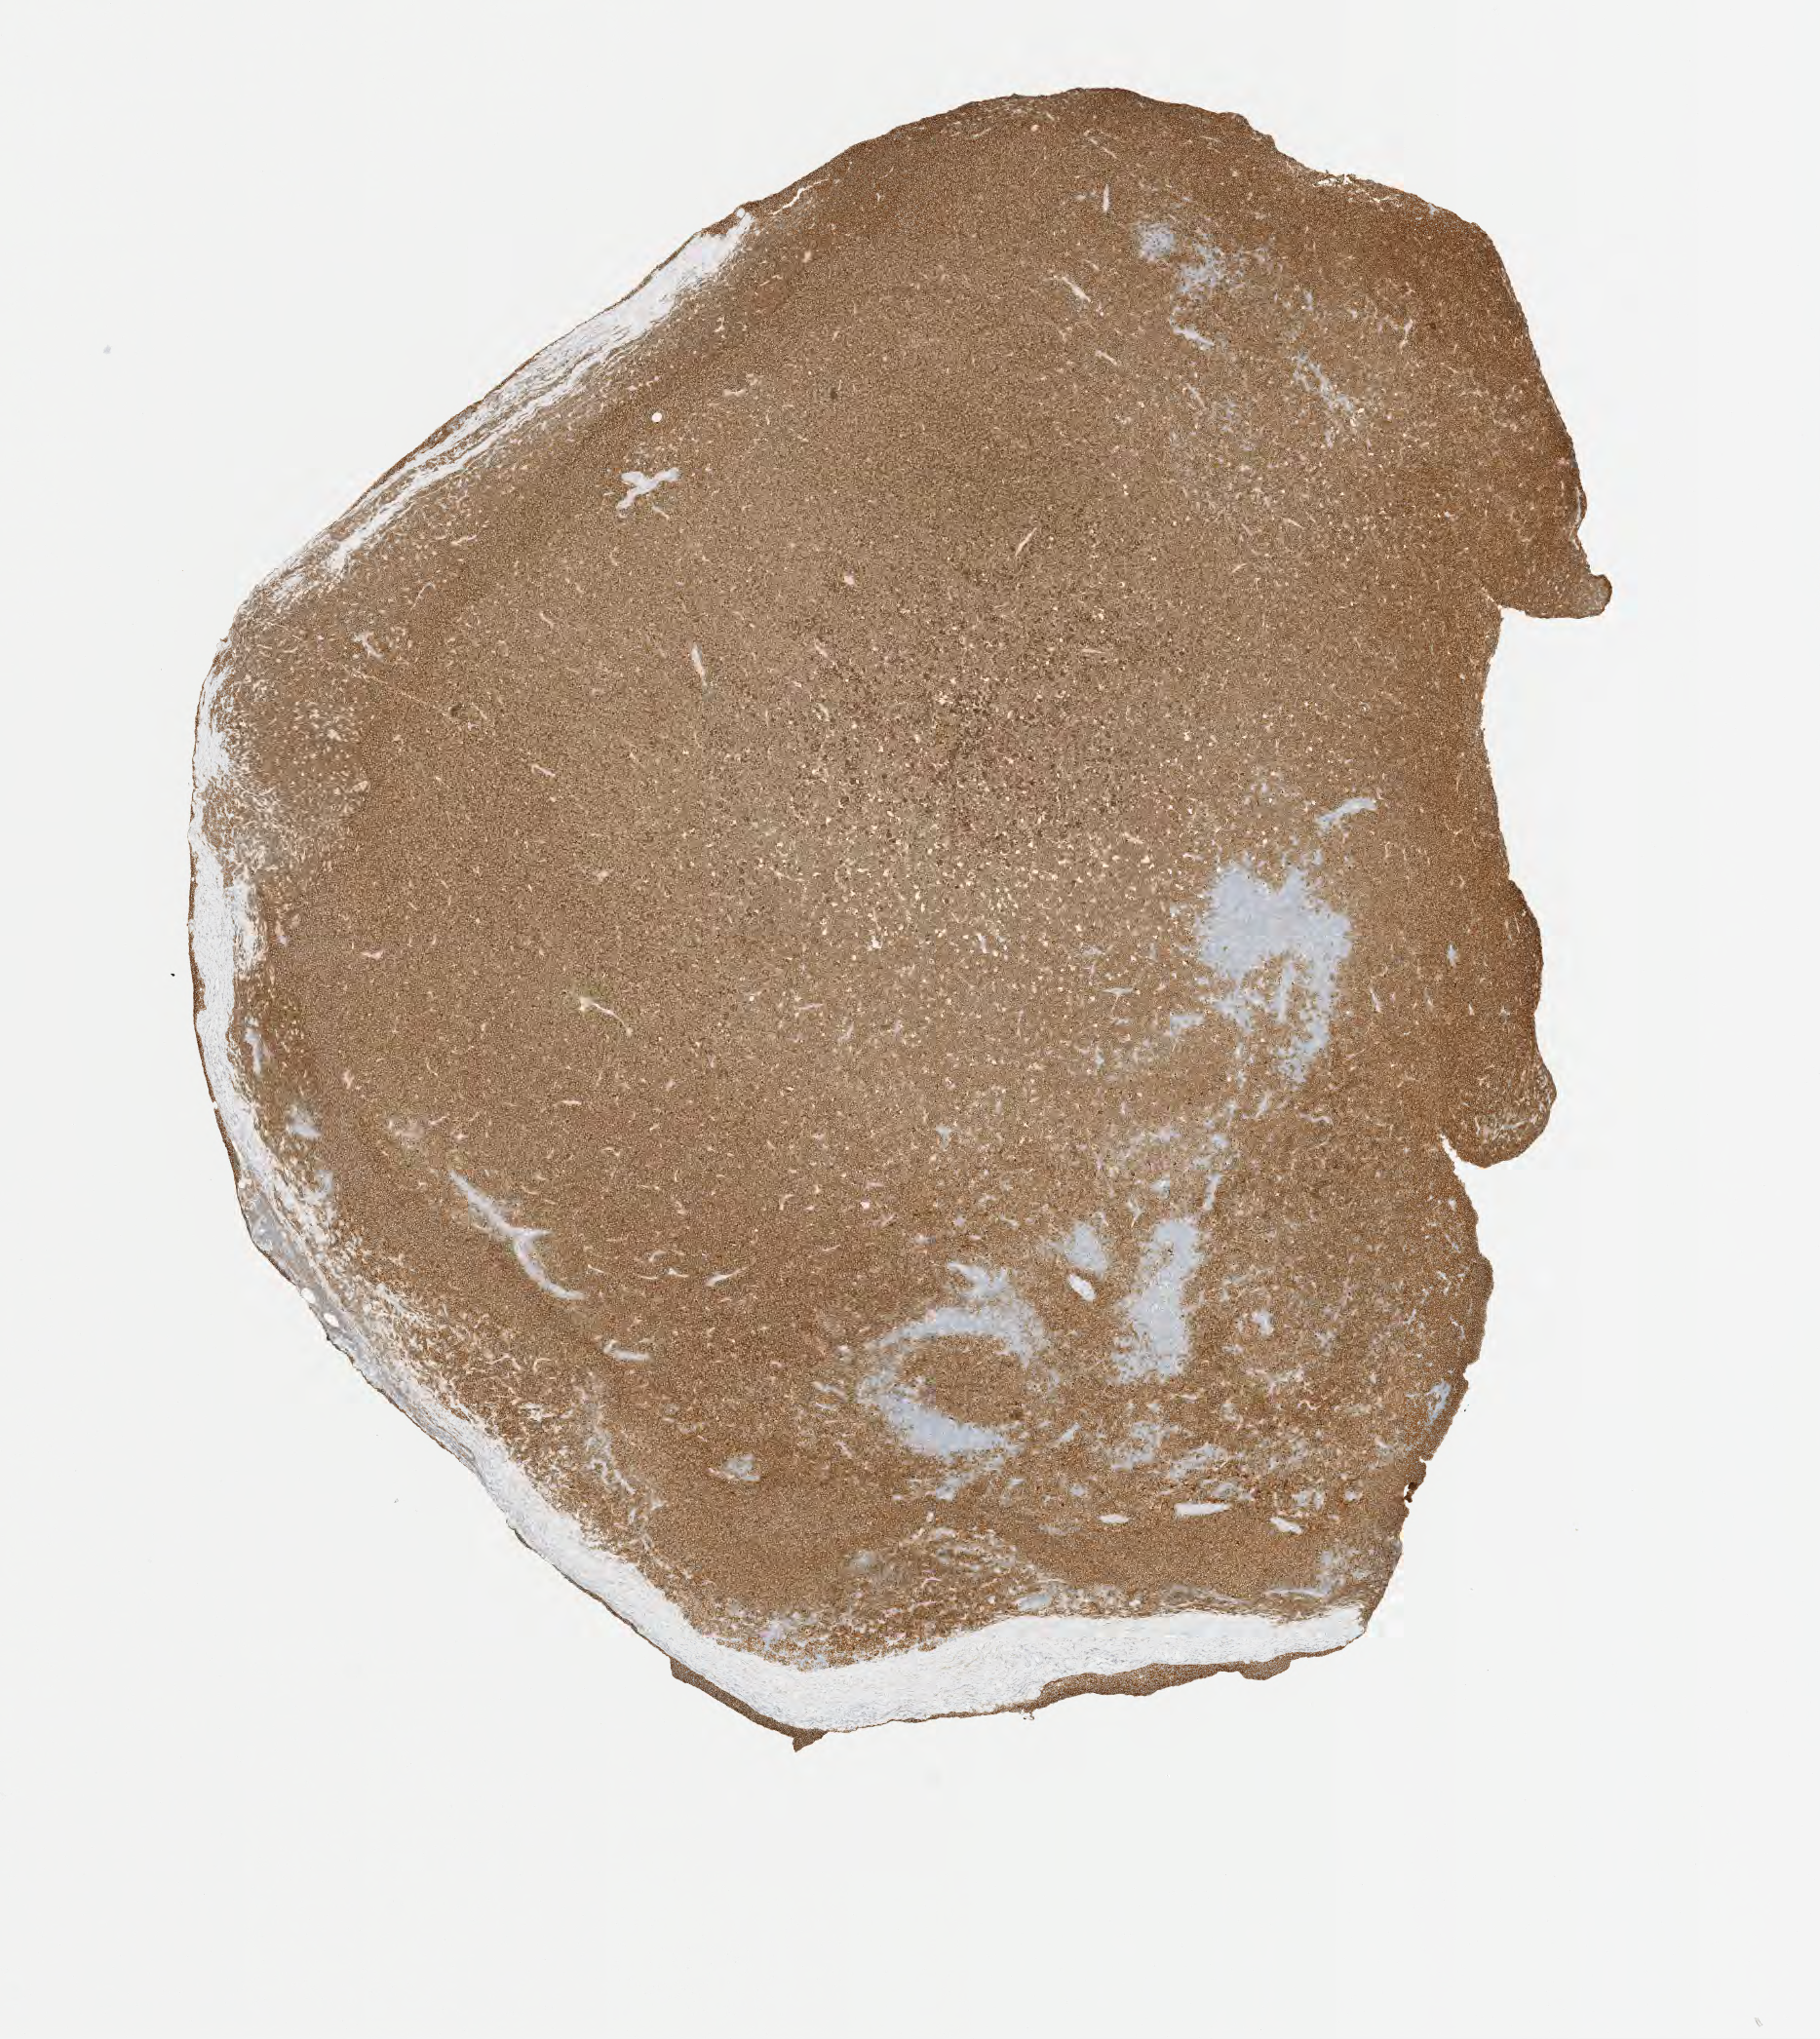
Immunohistochemistry (IHC) whole-slide image stained for CD10 — whole scanned area (about 7.6 x 8.5 mm) shown as a low-resolution overview; specimen: tumor tissue. Patient male; aged 45.
- diagnosis: Burkitt lymphoma, NOS